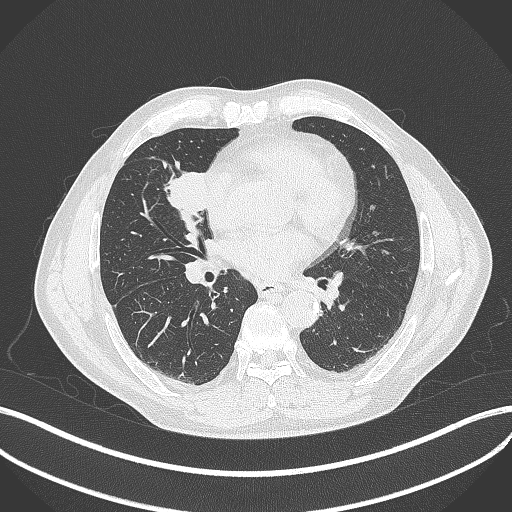
Chest CT, one axial slice; reconstruction kernel B70f; 120 kVp; lung window (W 1500 / L -600 HU); 1 mm slice thickness; 512 × 512 image matrix. Male patient, age 61 years. Case-level facts recorded for this patient, not image findings: clinical TNM (as recorded): T2b N1 M0.
Annotated regions visible in this slice (bounding box drawn by a radiologist):
- lung tumour (recorded histology: squamous cell carcinoma): box from (x=162, y=159) to (x=213, y=224) px